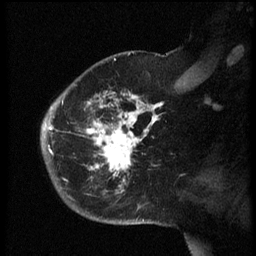
Breast MRI (dynamic contrast-enhanced), one sagittal slice; slice 43 of 60 in the series (ordered by position); dynamic contrast-enhanced series, image 2 of 3 at this slice position (ordered by acquisition); 1.5 T; TE 4.2 ms, TR 8.4 ms; 2.5 mm slice thickness; 256 × 256 image matrix, field of view 200 × 200 mm. Female patient, age 38 years. From the clinical record (not read from this slice): setting: breast cancer imaged before/during neoadjuvant chemotherapy; receptor status: HER2-positive.
Outlined on this slice (semi-automatically segmented with operator editing):
- analysis volume of interest (the breast-tissue region the enhancement analysis was run in; not a lesion): bounding box (x1, y1, x2, y2) in pixels: (42, 74, 165, 202)
- tumour enhancement mask (voxels above the 70 % enhancement threshold inside the analysis volume of interest): (45, 92, 164, 192)